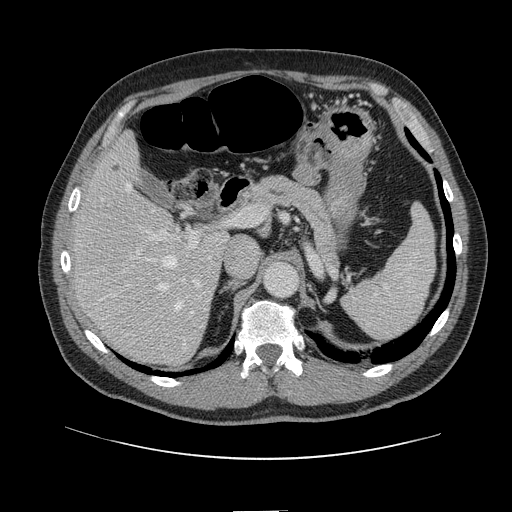
Contrast-enhanced abdominal CT, one axial slice. Position 85 of 161 along the scan axis. 120 kVp. Intravenous contrast given. Soft-tissue window (W 400 / L 40 HU). 2.5 mm slice thickness. 512 × 512 image matrix, field of view 412 × 412 mm. Male patient, age 66 years. From the clinical record (not read from this slice): diagnosis: colorectal cancer liver metastases, imaged before liver resection; multiple liver metastases: no; largest metastasis: 3.5 cm.
Outlined on this slice (outlined manually by an expert reader):
- hepatic veins: box from (x=101, y=183) to (x=184, y=311) px
- liver: (x=75, y=136)–(x=225, y=364)
- planned liver remnant (the part of the liver to remain after resection): (x=75, y=136)–(x=172, y=303)
- portal vein (with intrahepatic branches): (x=130, y=213)–(x=251, y=314)
- liver metastasis: (x=113, y=165)–(x=122, y=173)